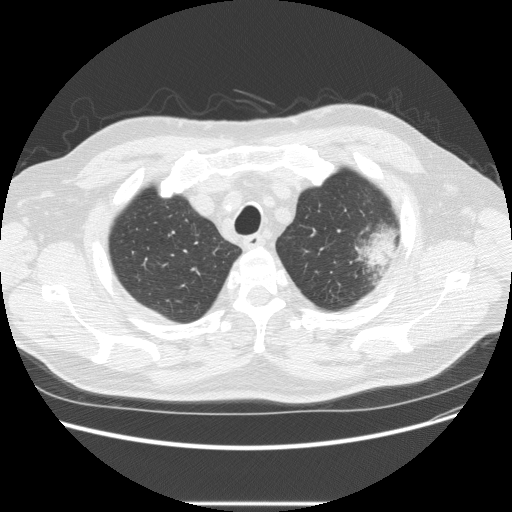
Low-dose screening chest CT, axial slice. First (baseline) screen. Lung window (W 1500 / L -600 HU). 2.5 mm slice thickness. Standard (soft-tissue) reconstruction kernel (STANDARD). 120 kVp. Slice 42 of 233 in the series. Male, age 73 years at enrolment.
Lesion marked by an expert reader, bounding box <332,216,407,283> (left, top, right, bottom; pixels). The screening reader recorded 2 non-calcified nodules or masses ≥4 mm on this exam (left upper lobe, right upper lobe); which of them this box marks is not recorded. Official screen result: positive, change unspecified: nodule(s) >= 4 mm or enlarging nodule(s), mass(es), or other non-specific abnormalities suspicious for lung cancer. Participant outcome: lung cancer diagnosed 11 days after this screen — bronchiolo-alveolar adenocarcinoma, NOS, other location, well differentiated (G1), stage IV (AJCC 6th edition).